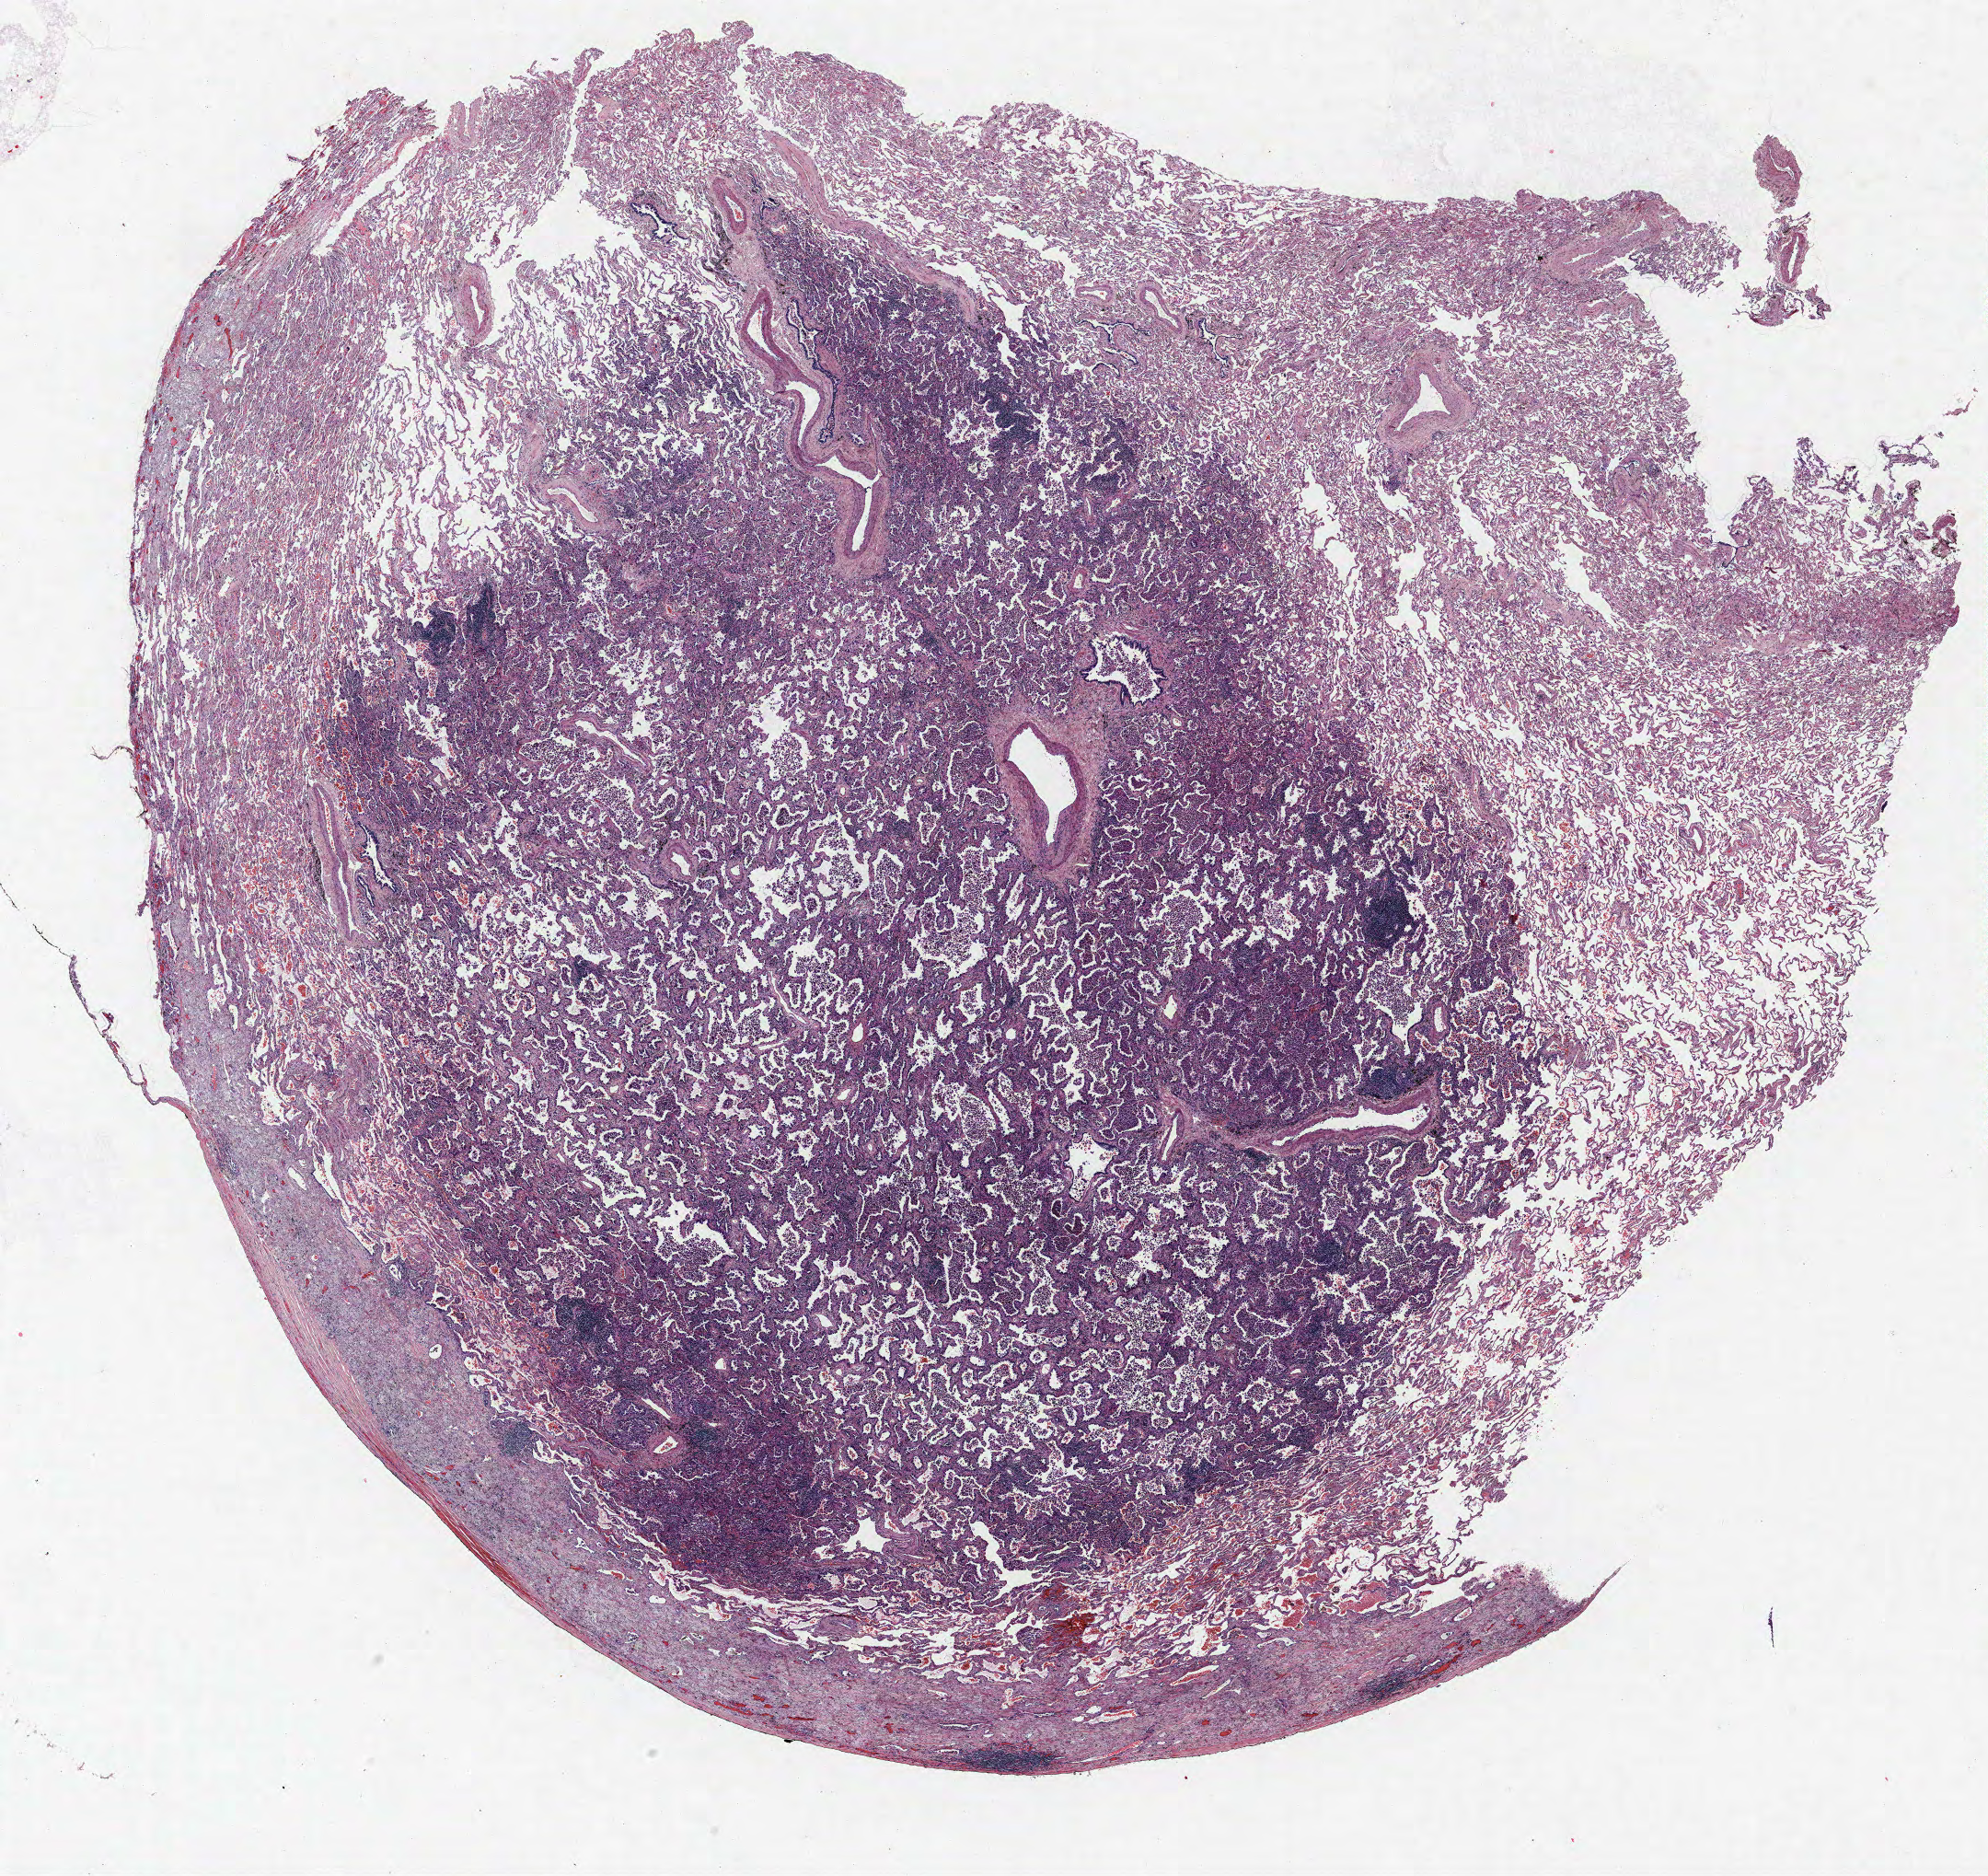
Hematoxylin and eosin (H&E) stained whole-slide image, shown as a low-resolution overview of the whole scanned area (about 17.3 x 16.3 mm, from a 40x scan); formalin-fixed paraffin-embedded (FFPE) section; lung tissue. Male patient, aged 74 at enrolment. Former smoker at enrolment.
Participant's lung-cancer diagnosis: Bronchiolo-alveolar carcinoma, non-mucinous.